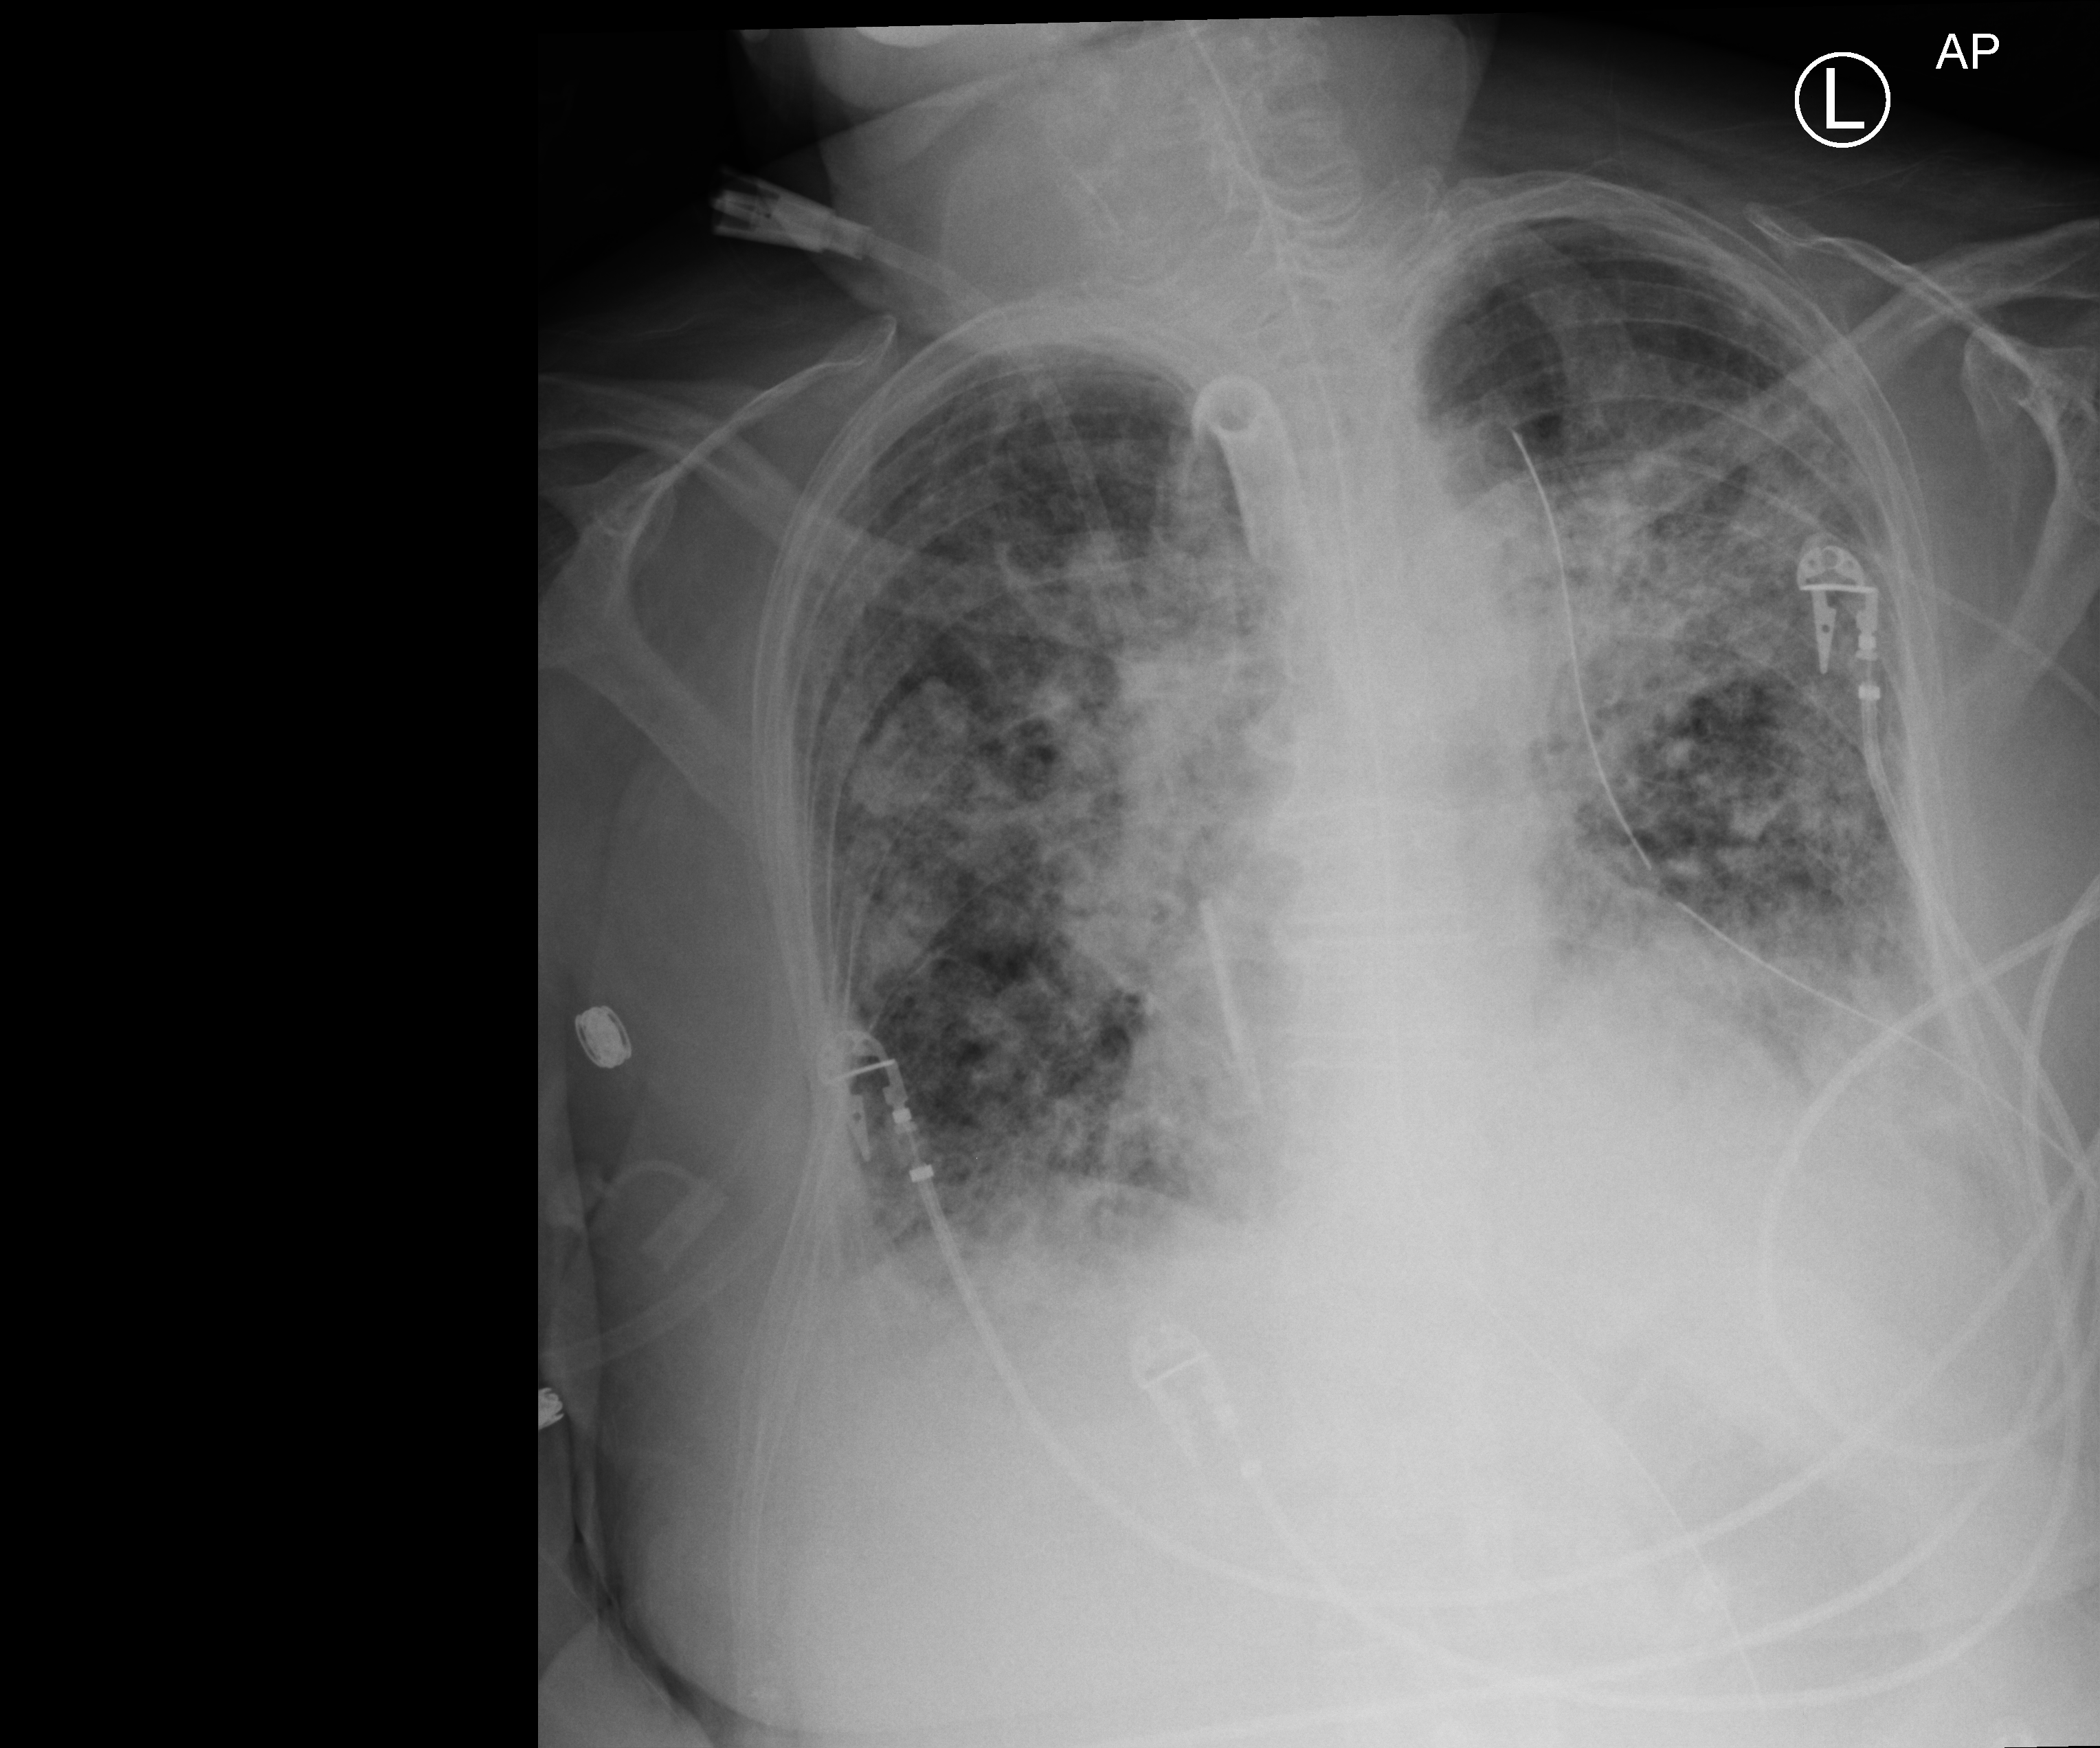
Chest X-ray (portable); anteroposterior (AP) projection. Patient hospitalised with COVID-19; female, aged 75–90 years.
Admission-level facts for this patient (not findings on this image; timing relative to this image not recorded):
- diabetes (admission record): no